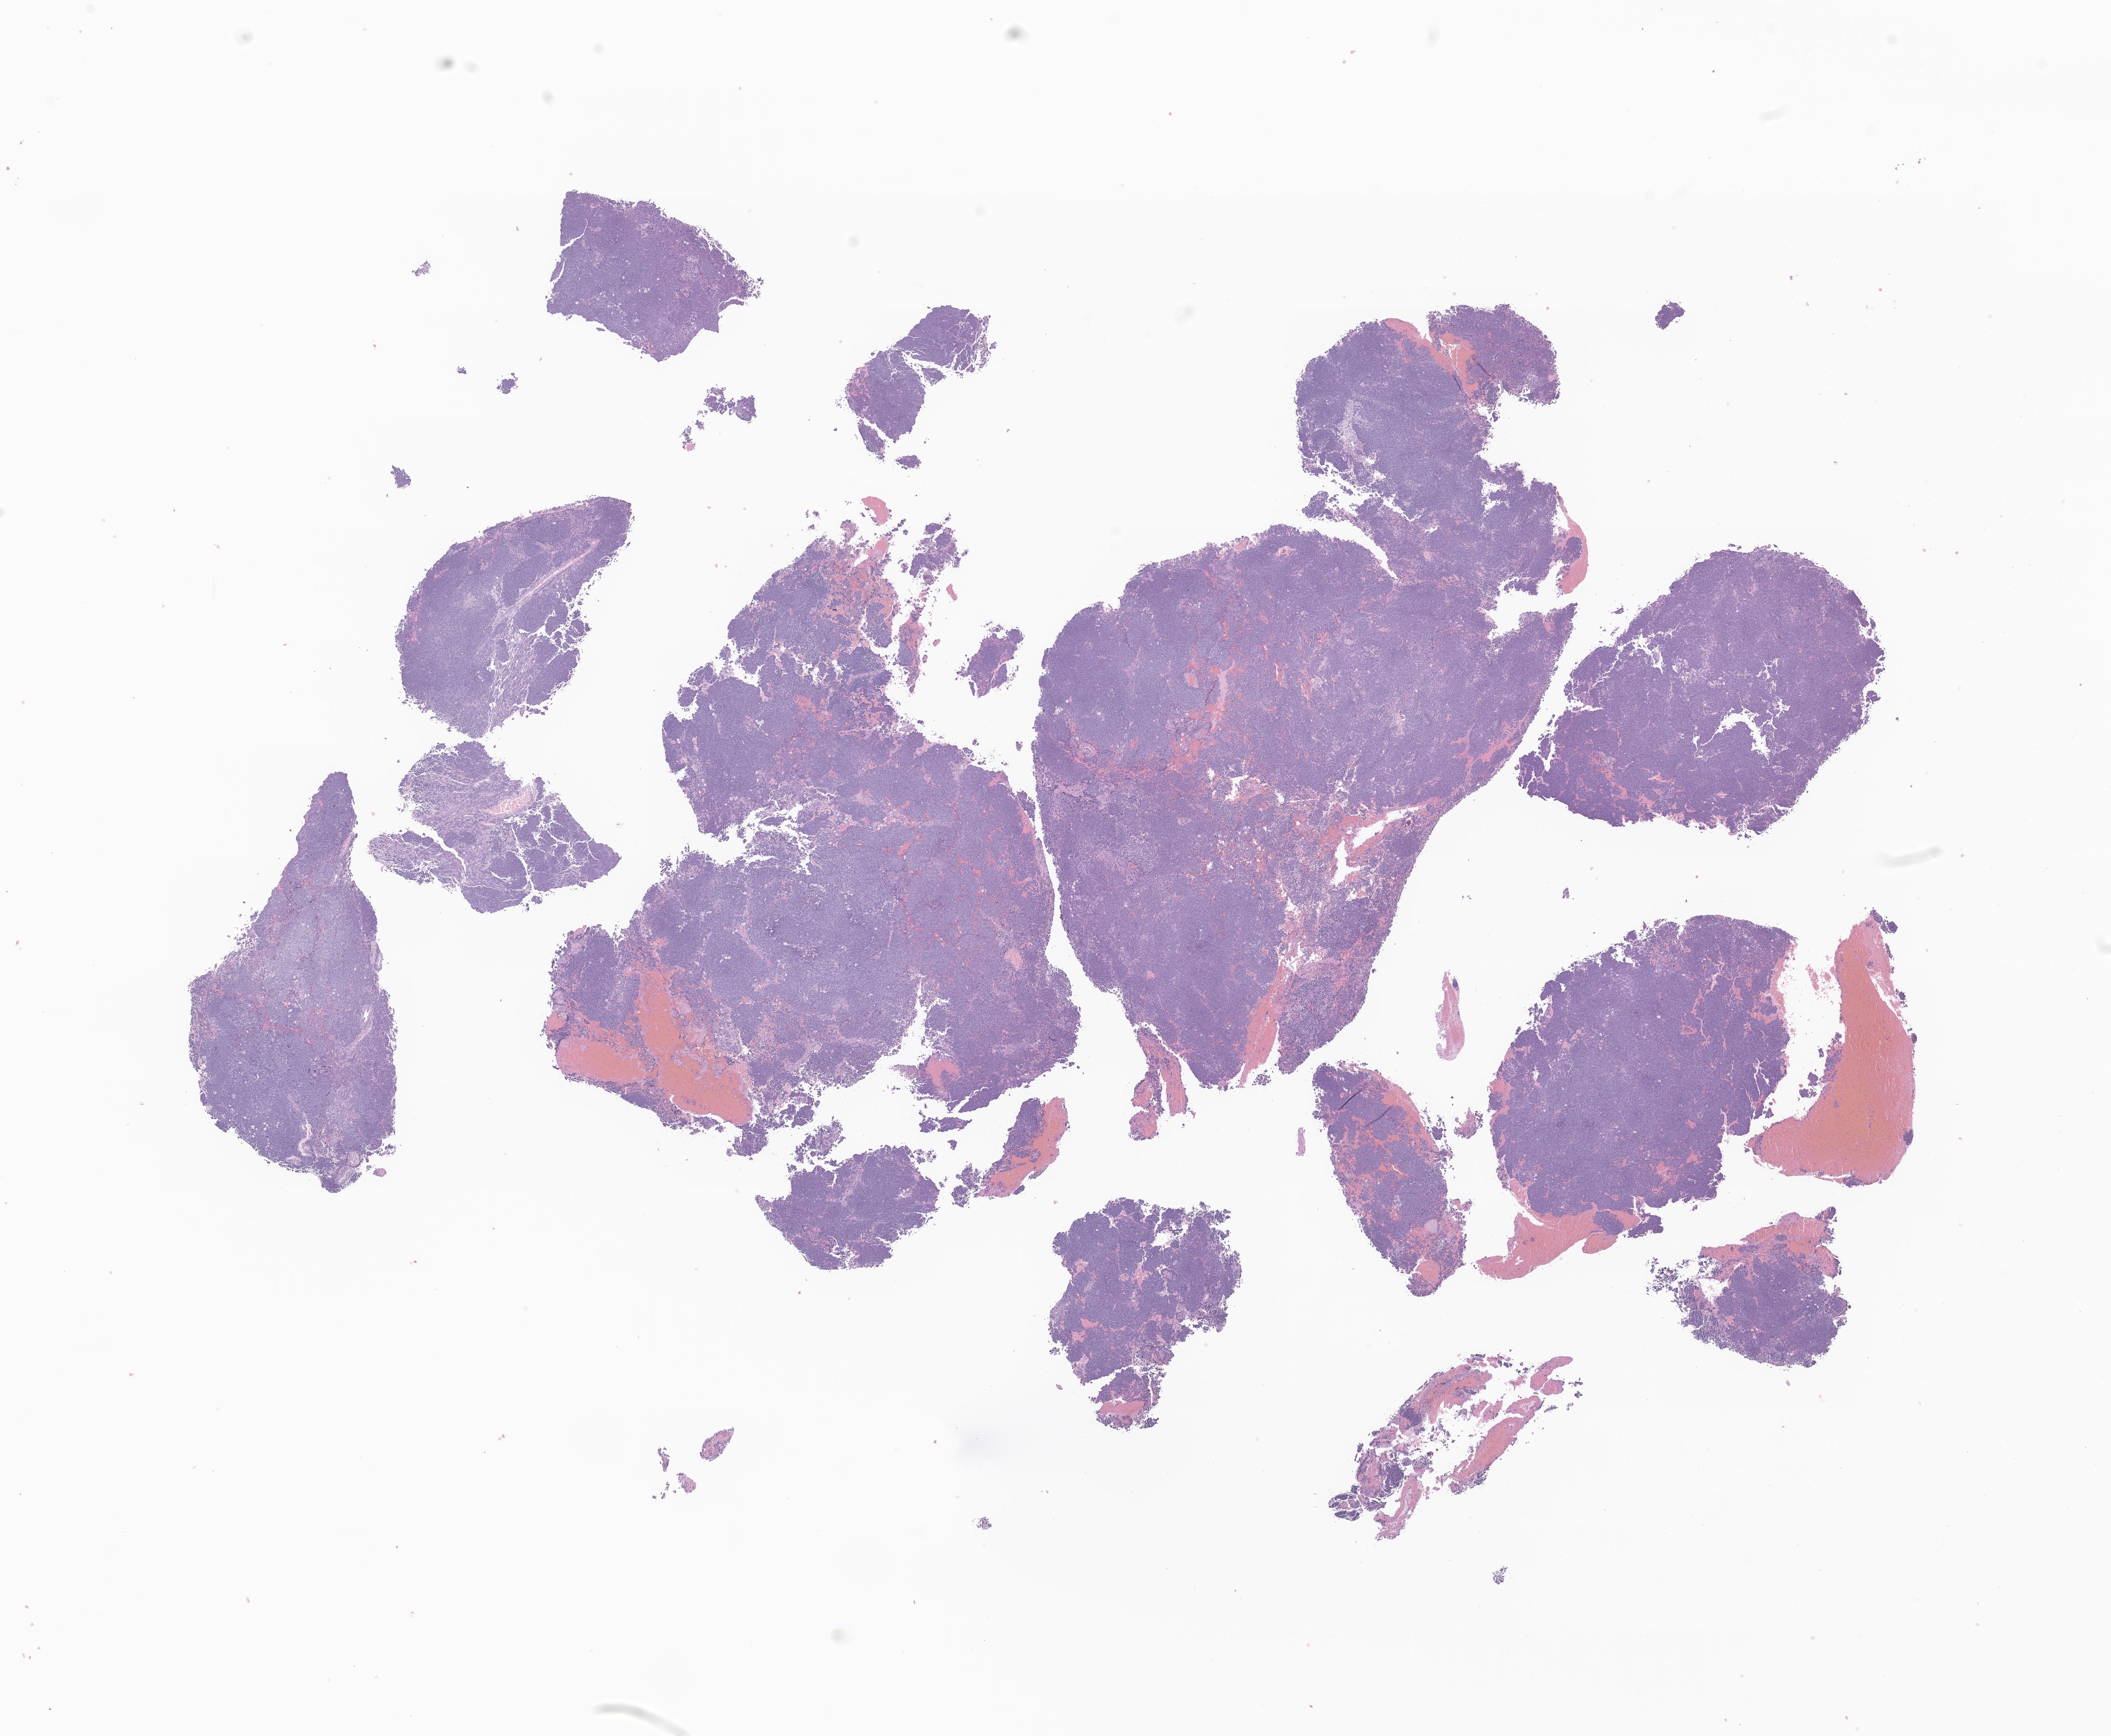
Digitized haematoxylin and eosin-stained section of tumor tissue from the brain — a low-resolution overview of the entire scanned area, about 20.5 x 16.8 mm. Formalin-fixed paraffin-embedded section. Patient male; age 158 months (13 years 2 months).
Diagnosis (ICD-O-3 morphology term): Medulloblastoma, NOS.